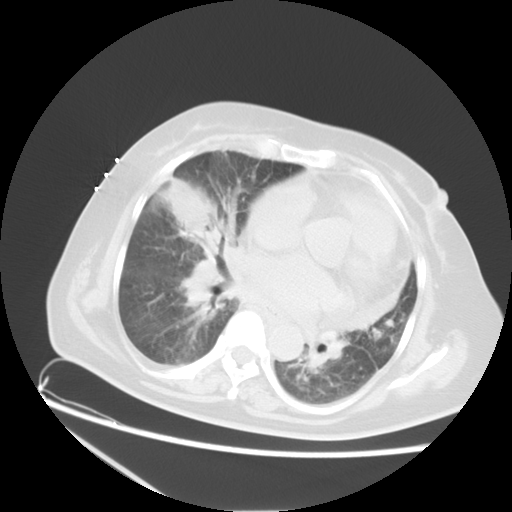
Chest CT, one axial slice. Slice 10 of 22 in the series (ordered by position). Reconstruction kernel STANDARD. 120 kVp. Lung window (W 1500 / L -600 HU). 5 mm slice thickness. 512 × 512 image matrix, field of view 350 × 350 mm. Patient: female, 67 years. From the clinical record (not read from this slice): clinical TNM (as recorded): T2a N3 M1a.
Structures marked on this image (bounding box drawn by a radiologist):
- lung tumour (recorded histology: adenocarcinoma): bounding box <162,174,211,239> (left, top, right, bottom; pixels)